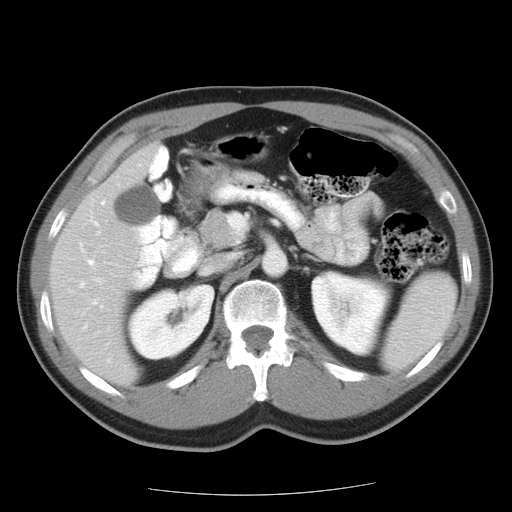
Contrast-enhanced abdominal CT, one axial slice. Position 8 of 22 along the scan axis. 120 kVp. Soft-tissue window (W 400 / L 40 HU). 7.5 mm slice thickness. 512 × 512 image matrix, field of view 359 × 359 mm. Male patient, age 41 years. Case-level facts recorded for this patient, not image findings: diagnosis: colorectal cancer liver metastases, imaged before liver resection; multiple liver metastases: no; largest metastasis: 2.7 cm; chemotherapy before resection: no.
Outlined on this slice (manually delineated by an expert):
- hepatic veins: bounding box [x1, y1, x2, y2] px = [81, 202, 106, 305]
- liver: [53, 149, 153, 380]
- planned liver remnant (the part of the liver to remain after resection): [53, 149, 153, 379]
- portal vein (with intrahepatic branches): [98, 233, 100, 235]